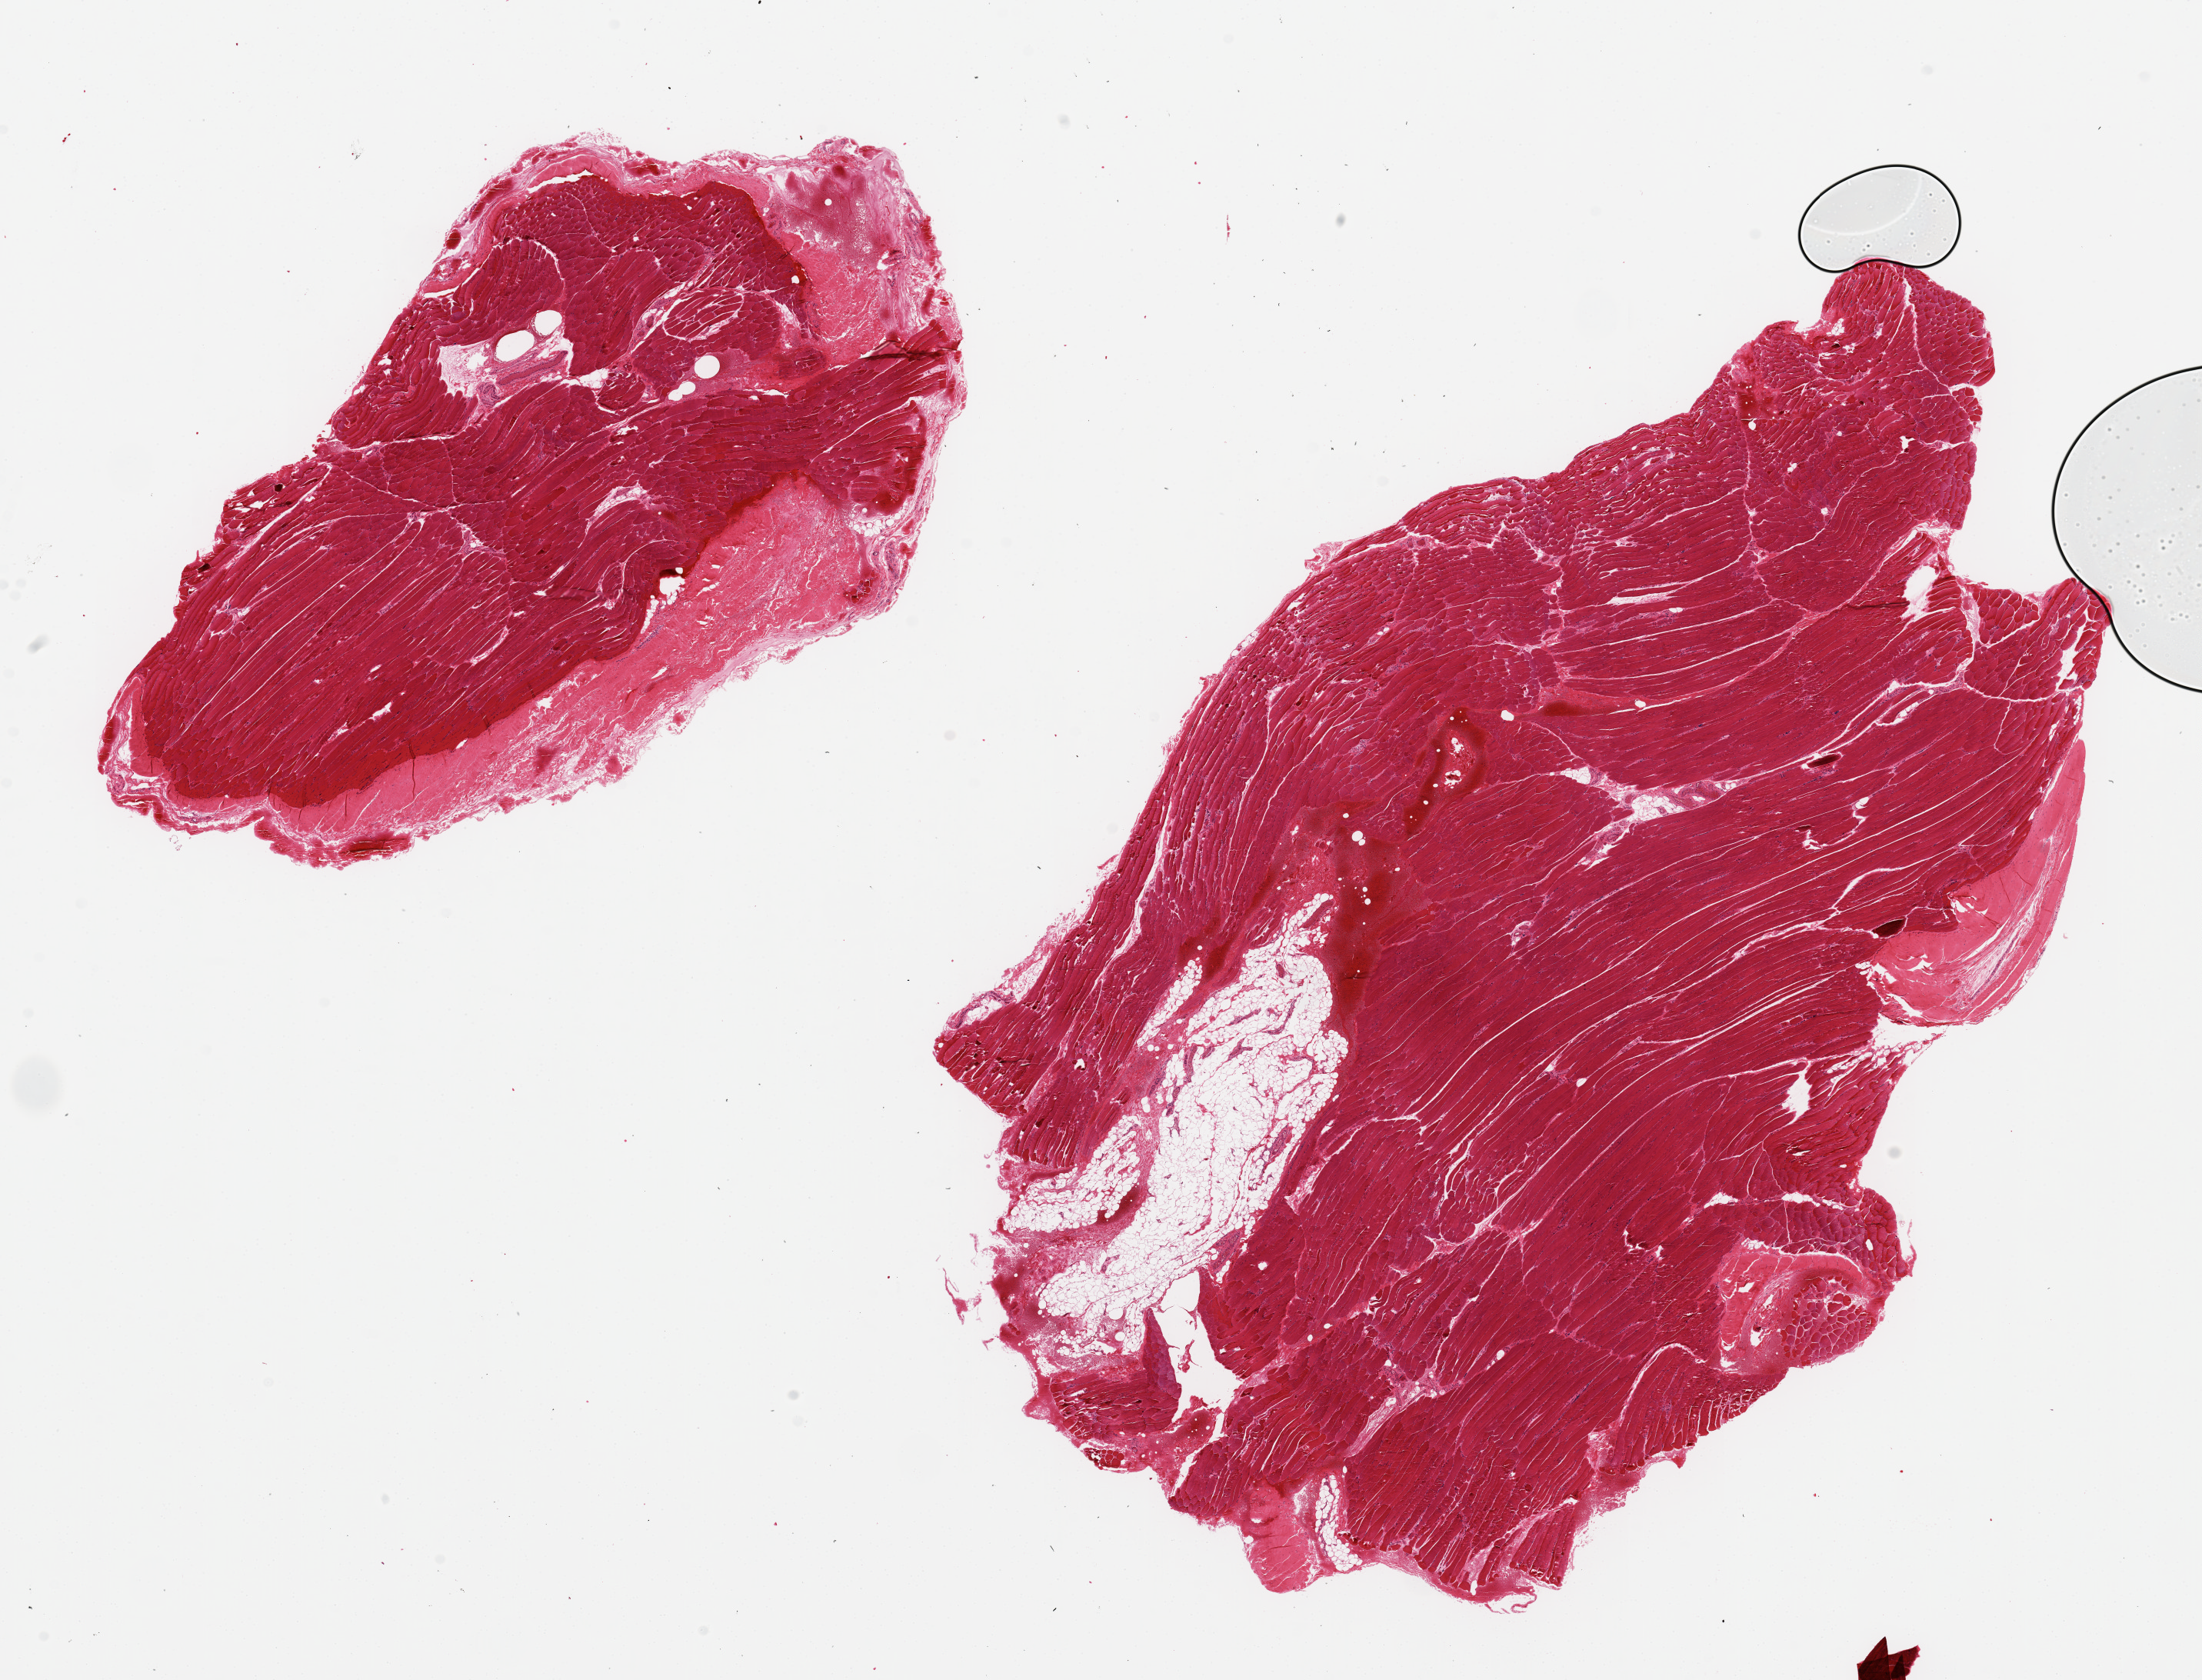
H&E whole-slide image — a low-resolution overview of the entire scanned area, about 22.6 x 17.3 mm (from a 20x scan). PAXgene-fixed paraffin-embedded (PFPE) section. Target tissue: skeletal muscle. Tissue donor sample. Male donor.
- reviewer comment on this tissue sample: 2 pieces ~12x8mm. Intertitial fat/fibrous scar tissue is ~10% of specimens